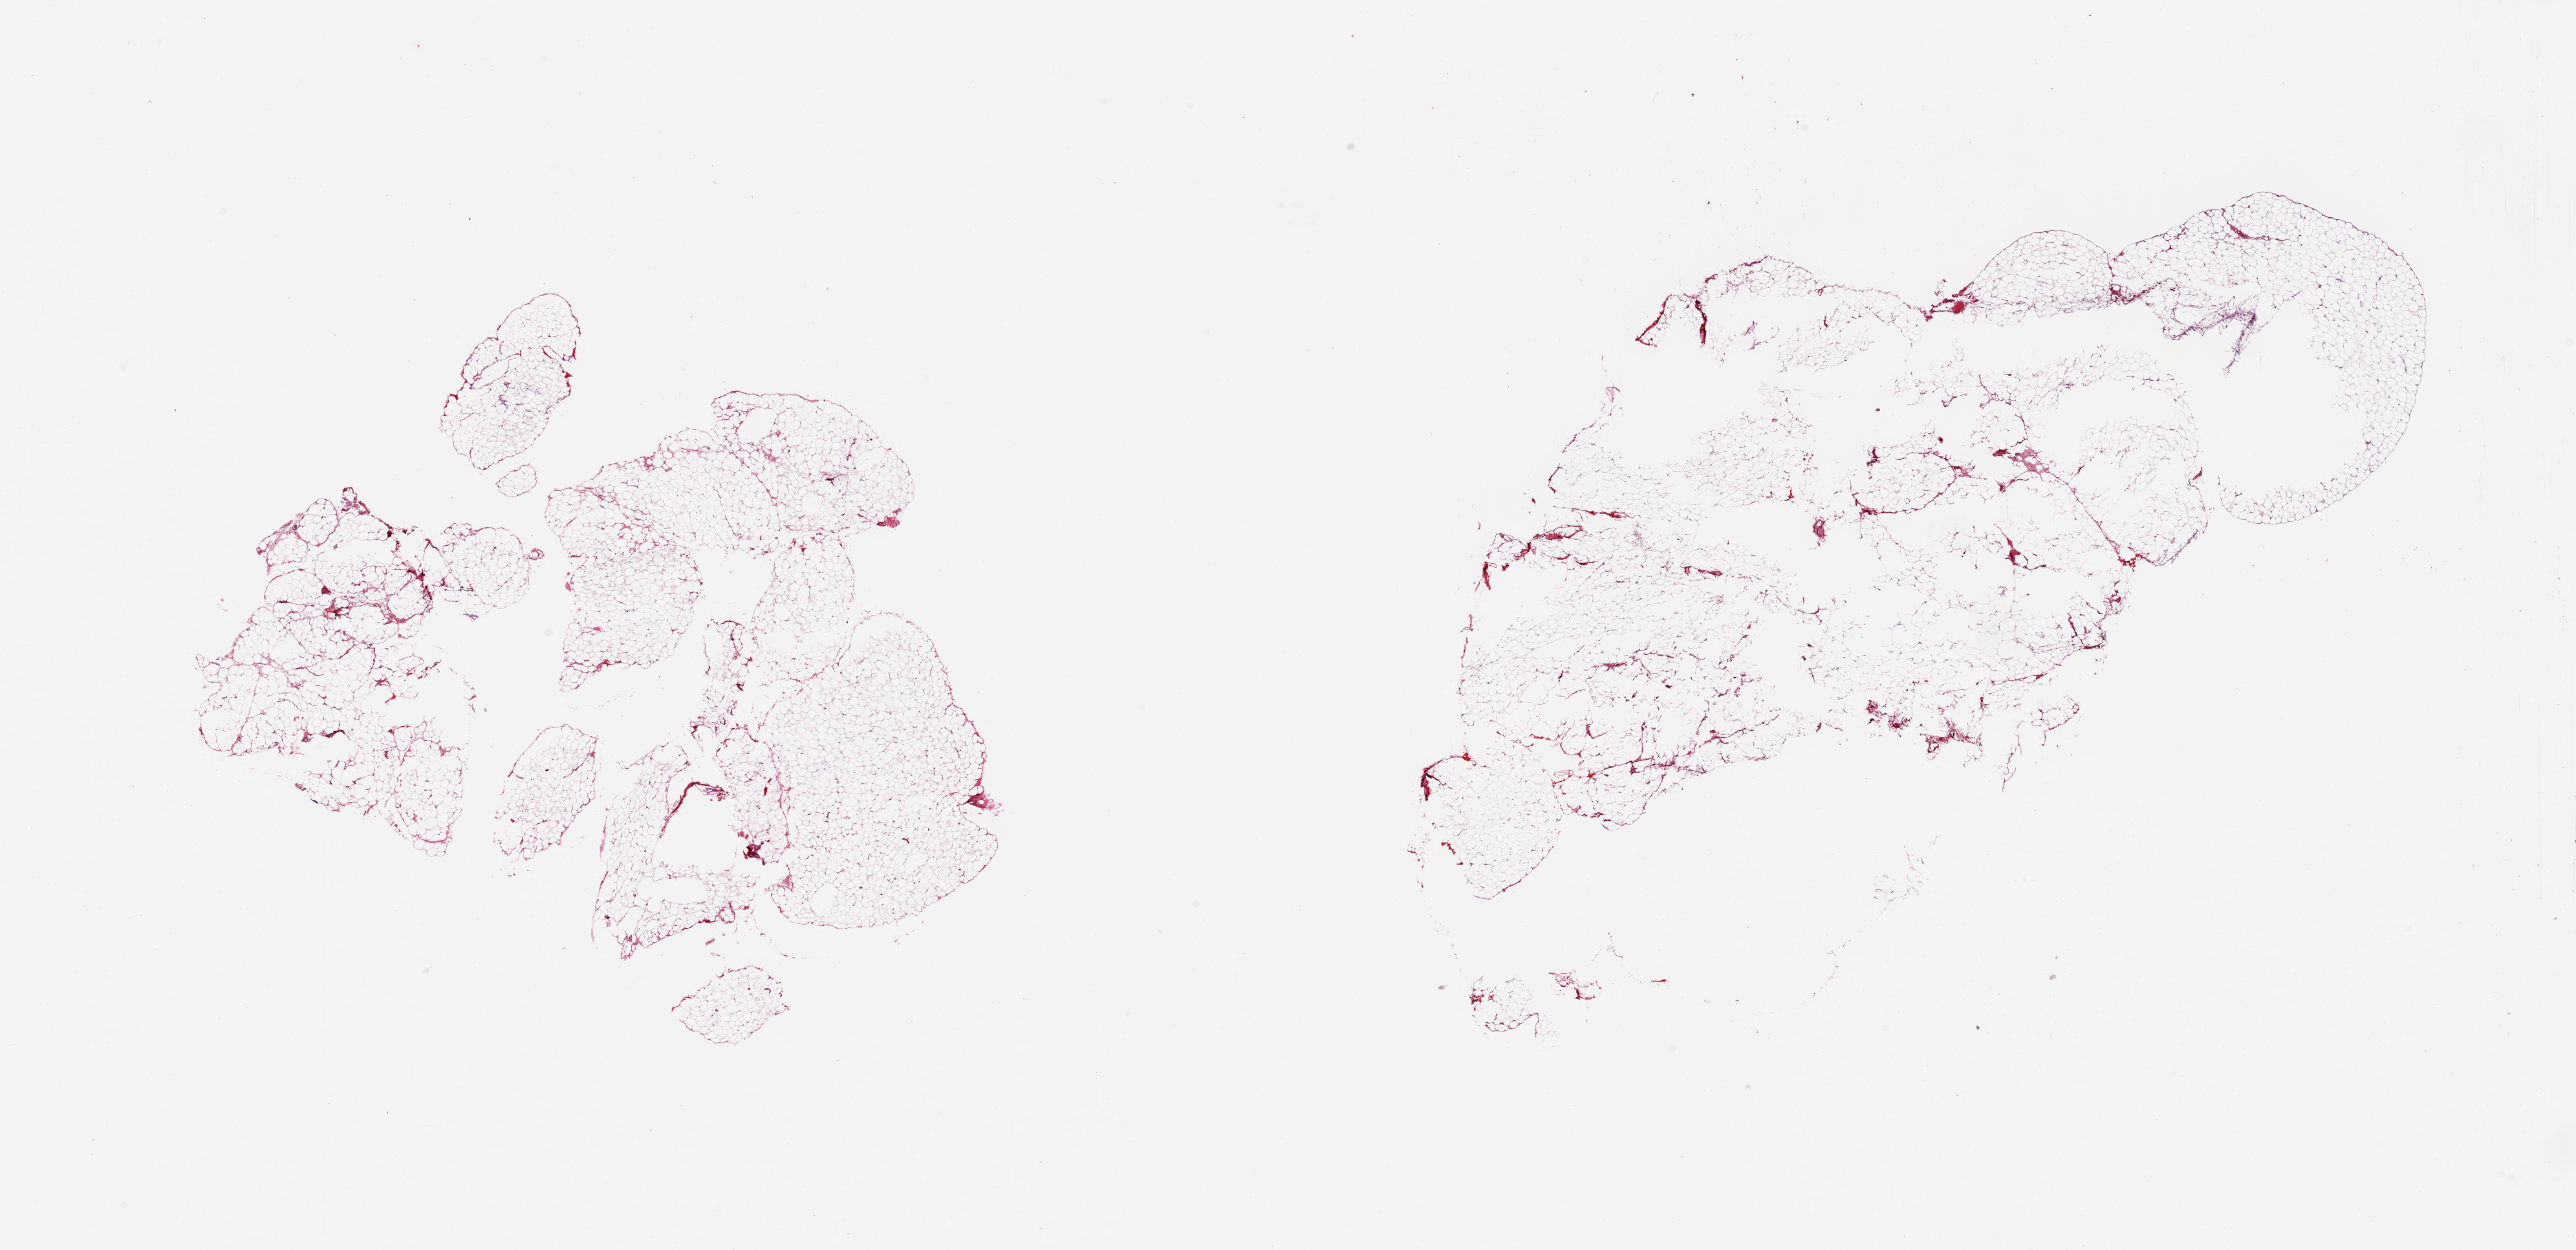
Whole-slide image, H&E stain, a low-resolution overview of the entire scanned area, about 31.5 x 15.3 mm; PAXgene-fixed paraffin-embedded (PFPE) section; sampled site (target tissue): omentum; donor tissue sample. Donor sex: male.
Reviewer comment on this tissue sample: 2 pieces, no abnormalities.